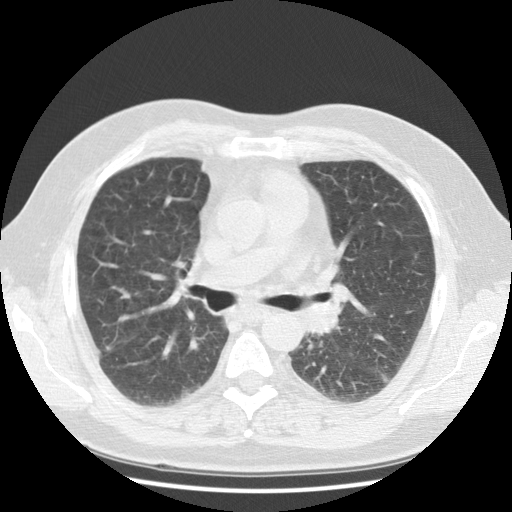
Low-dose screening chest CT, one axial slice. Position 67 of 108 along the scan axis. Reconstruction kernel STANDARD. Lung window (W 1500 / L -600 HU). 2.5 mm slice thickness. 512 × 512 image matrix, field of view 350 × 350 mm.
Annotated regions visible in this slice (outlined manually by an expert reader):
- lesion 1 (tumor, hilum of left lung): bounding box <307,302,339,334> (left, top, right, bottom; pixels)